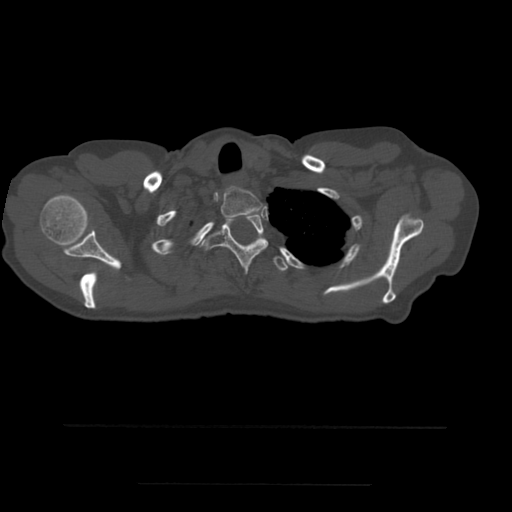
CT including the spine, one axial slice; slice 435 of 544 in the series (ordered by position); bone window (W 1800 / L 400 HU); 1.25 mm slice thickness; 512 × 512 image matrix, field of view 350 × 350 mm. Patient age 58 years. From the clinical record (not read from this slice): primary cancer: lung.
Outlined on this slice (semi-automatically segmented with operator editing):
- T1 vertebra: box from (x=221, y=187) to (x=263, y=218) px
- T2 vertebra: (x=201, y=211)–(x=269, y=273)
- T3 vertebra: (x=274, y=257)–(x=288, y=272)